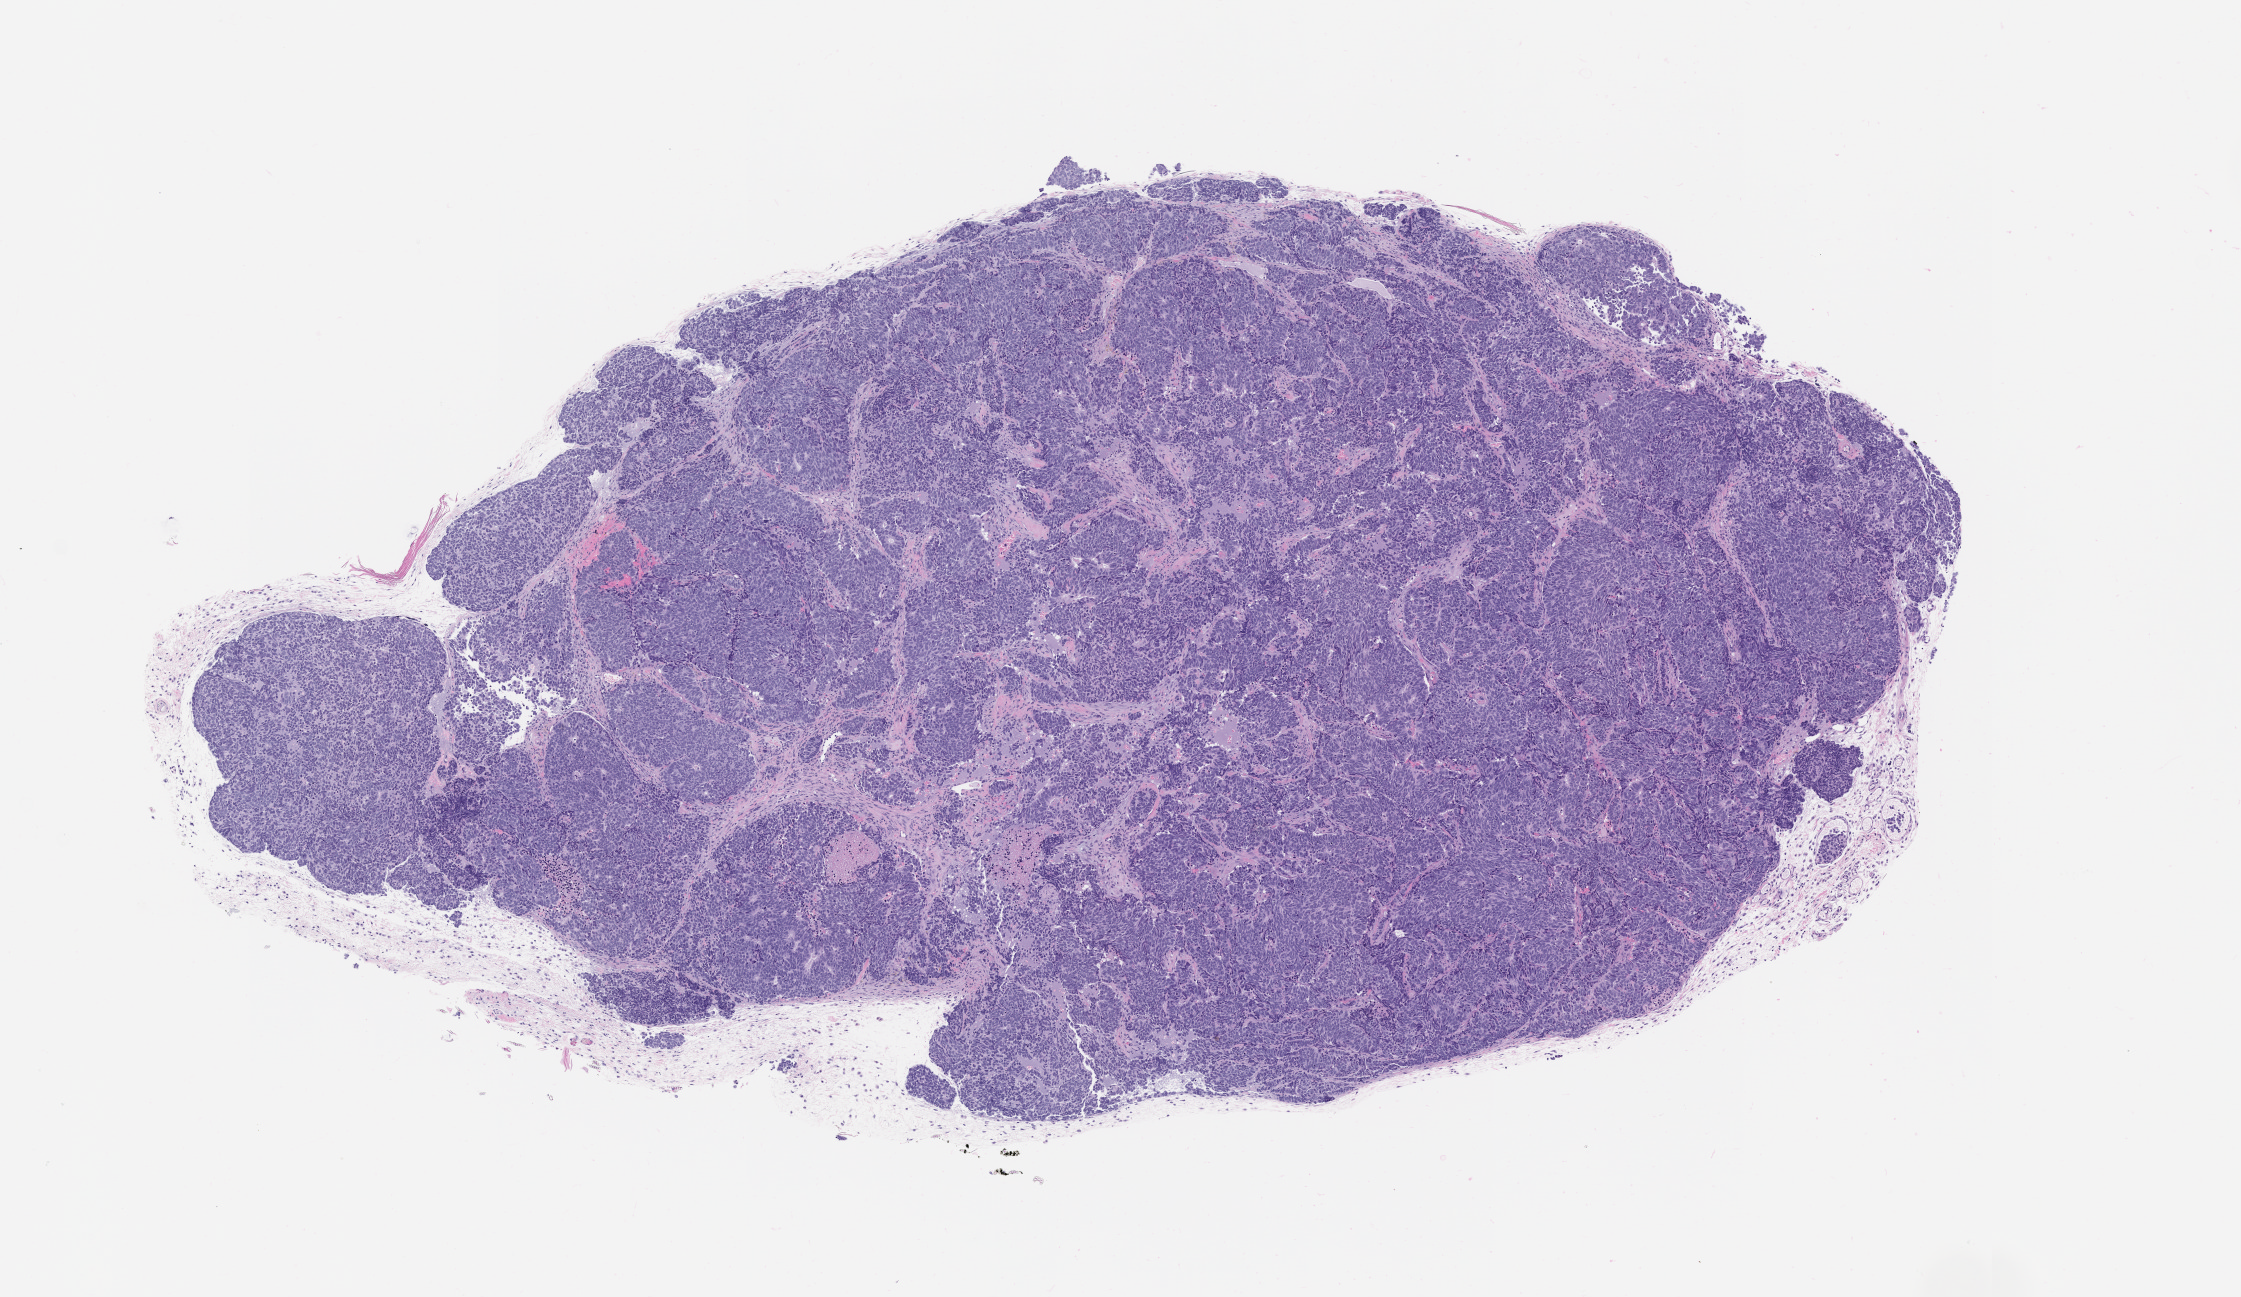
H&E whole-slide image of a patient-derived xenograft (PDX) tumor grown in a mouse, passage 1 — whole scanned area (about 9.0 x 5.2 mm) shown as a low-resolution overview, formalin-fixed paraffin-embedded section, tumor site category: bladder.
* originating patient diagnosis: Bladder Small Cell Neuroendocrine Carcinoma